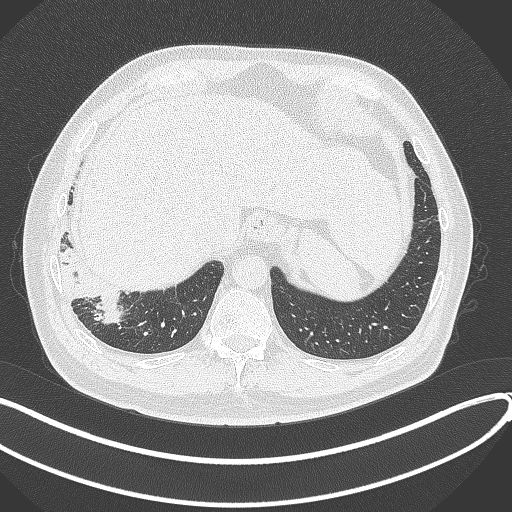
Chest CT, one axial slice. Slice 56 of 360 in the series (ordered by position). Reconstruction kernel B70f. Lung window (W 1500 / L -600 HU). 512 × 512 image matrix, field of view 400 × 400 mm. Patient: male, 59 years.
Outlined on this slice (rectangle marked by the reading radiologist):
- lung tumour (recorded histology: adenocarcinoma): bounding box [x1, y1, x2, y2] px = [63, 255, 122, 327]